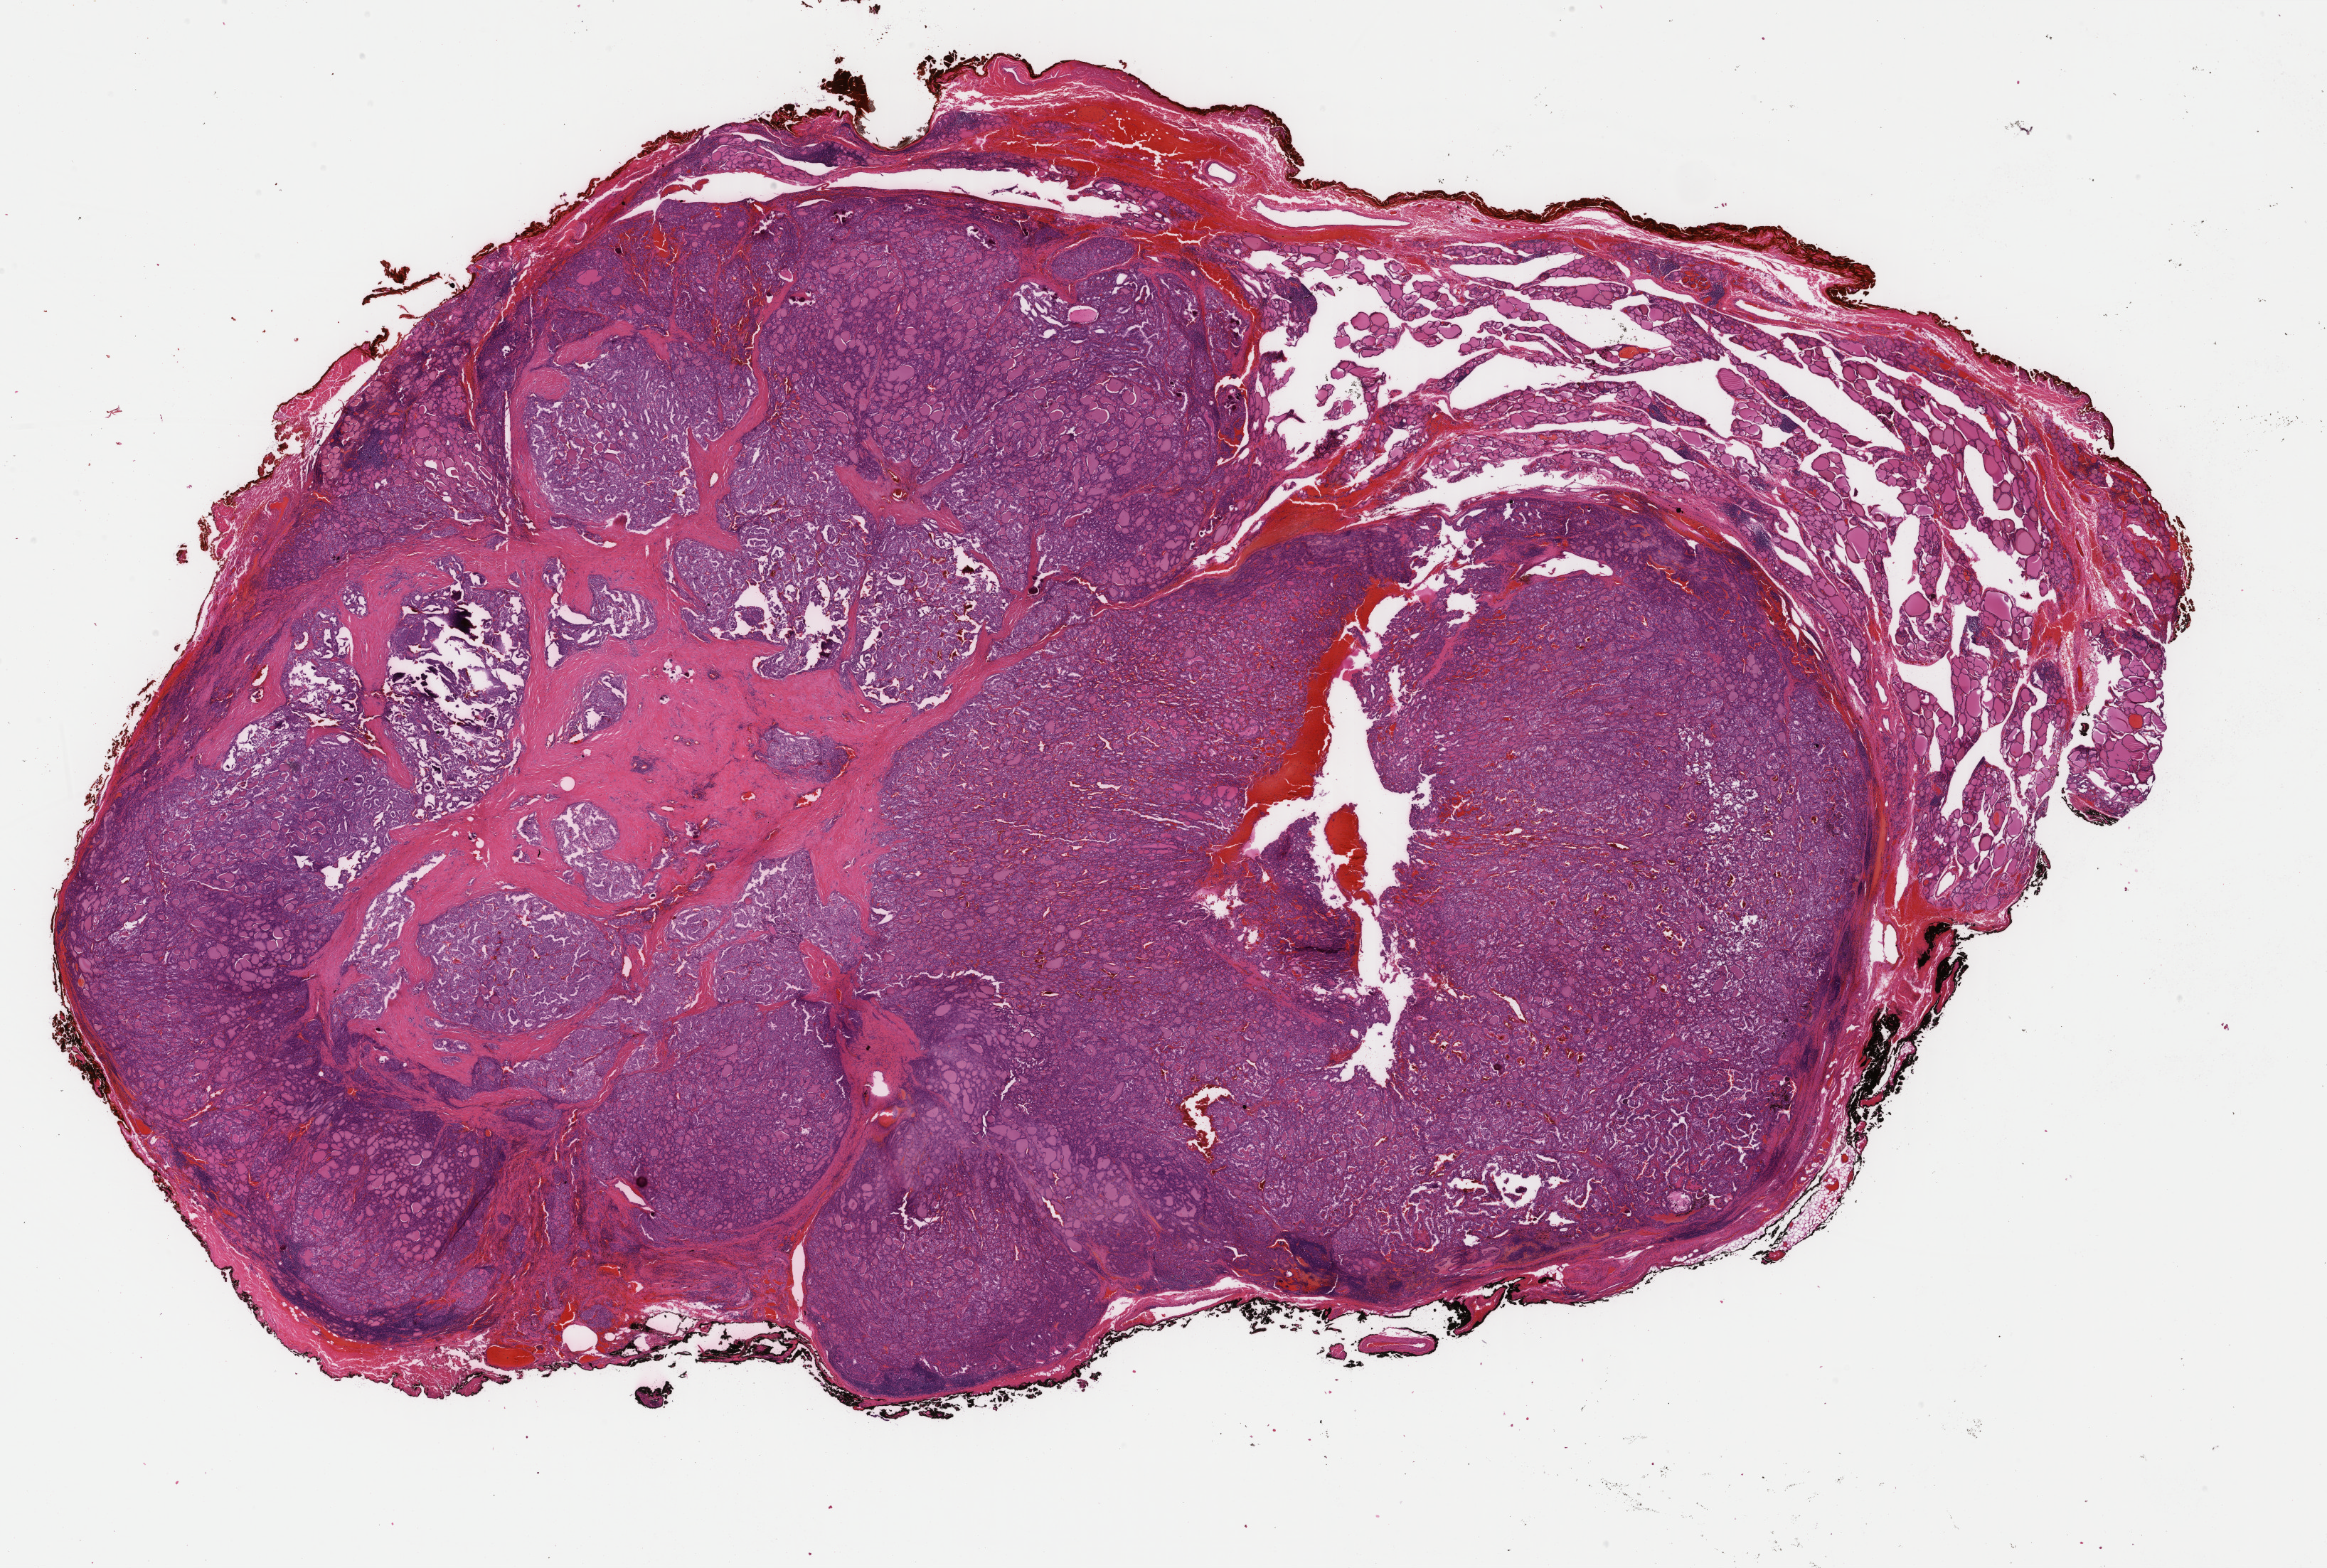
Digitized H&E-stained tissue section (whole slide) — whole scanned area (about 26.0 x 17.5 mm, from a 40x scan) shown as a low-resolution overview. Formalin-fixed paraffin-embedded (FFPE) diagnostic section. Thyroid, primary tumour sample. Patient: female, age at initial diagnosis 24 years.
Histologic diagnosis: Papillary carcinoma, follicular variant (thyroid gland). Lymph nodes positive (case pathology): 7 of 20 examined. Laterality: left. AJCC pathologic stage: I.